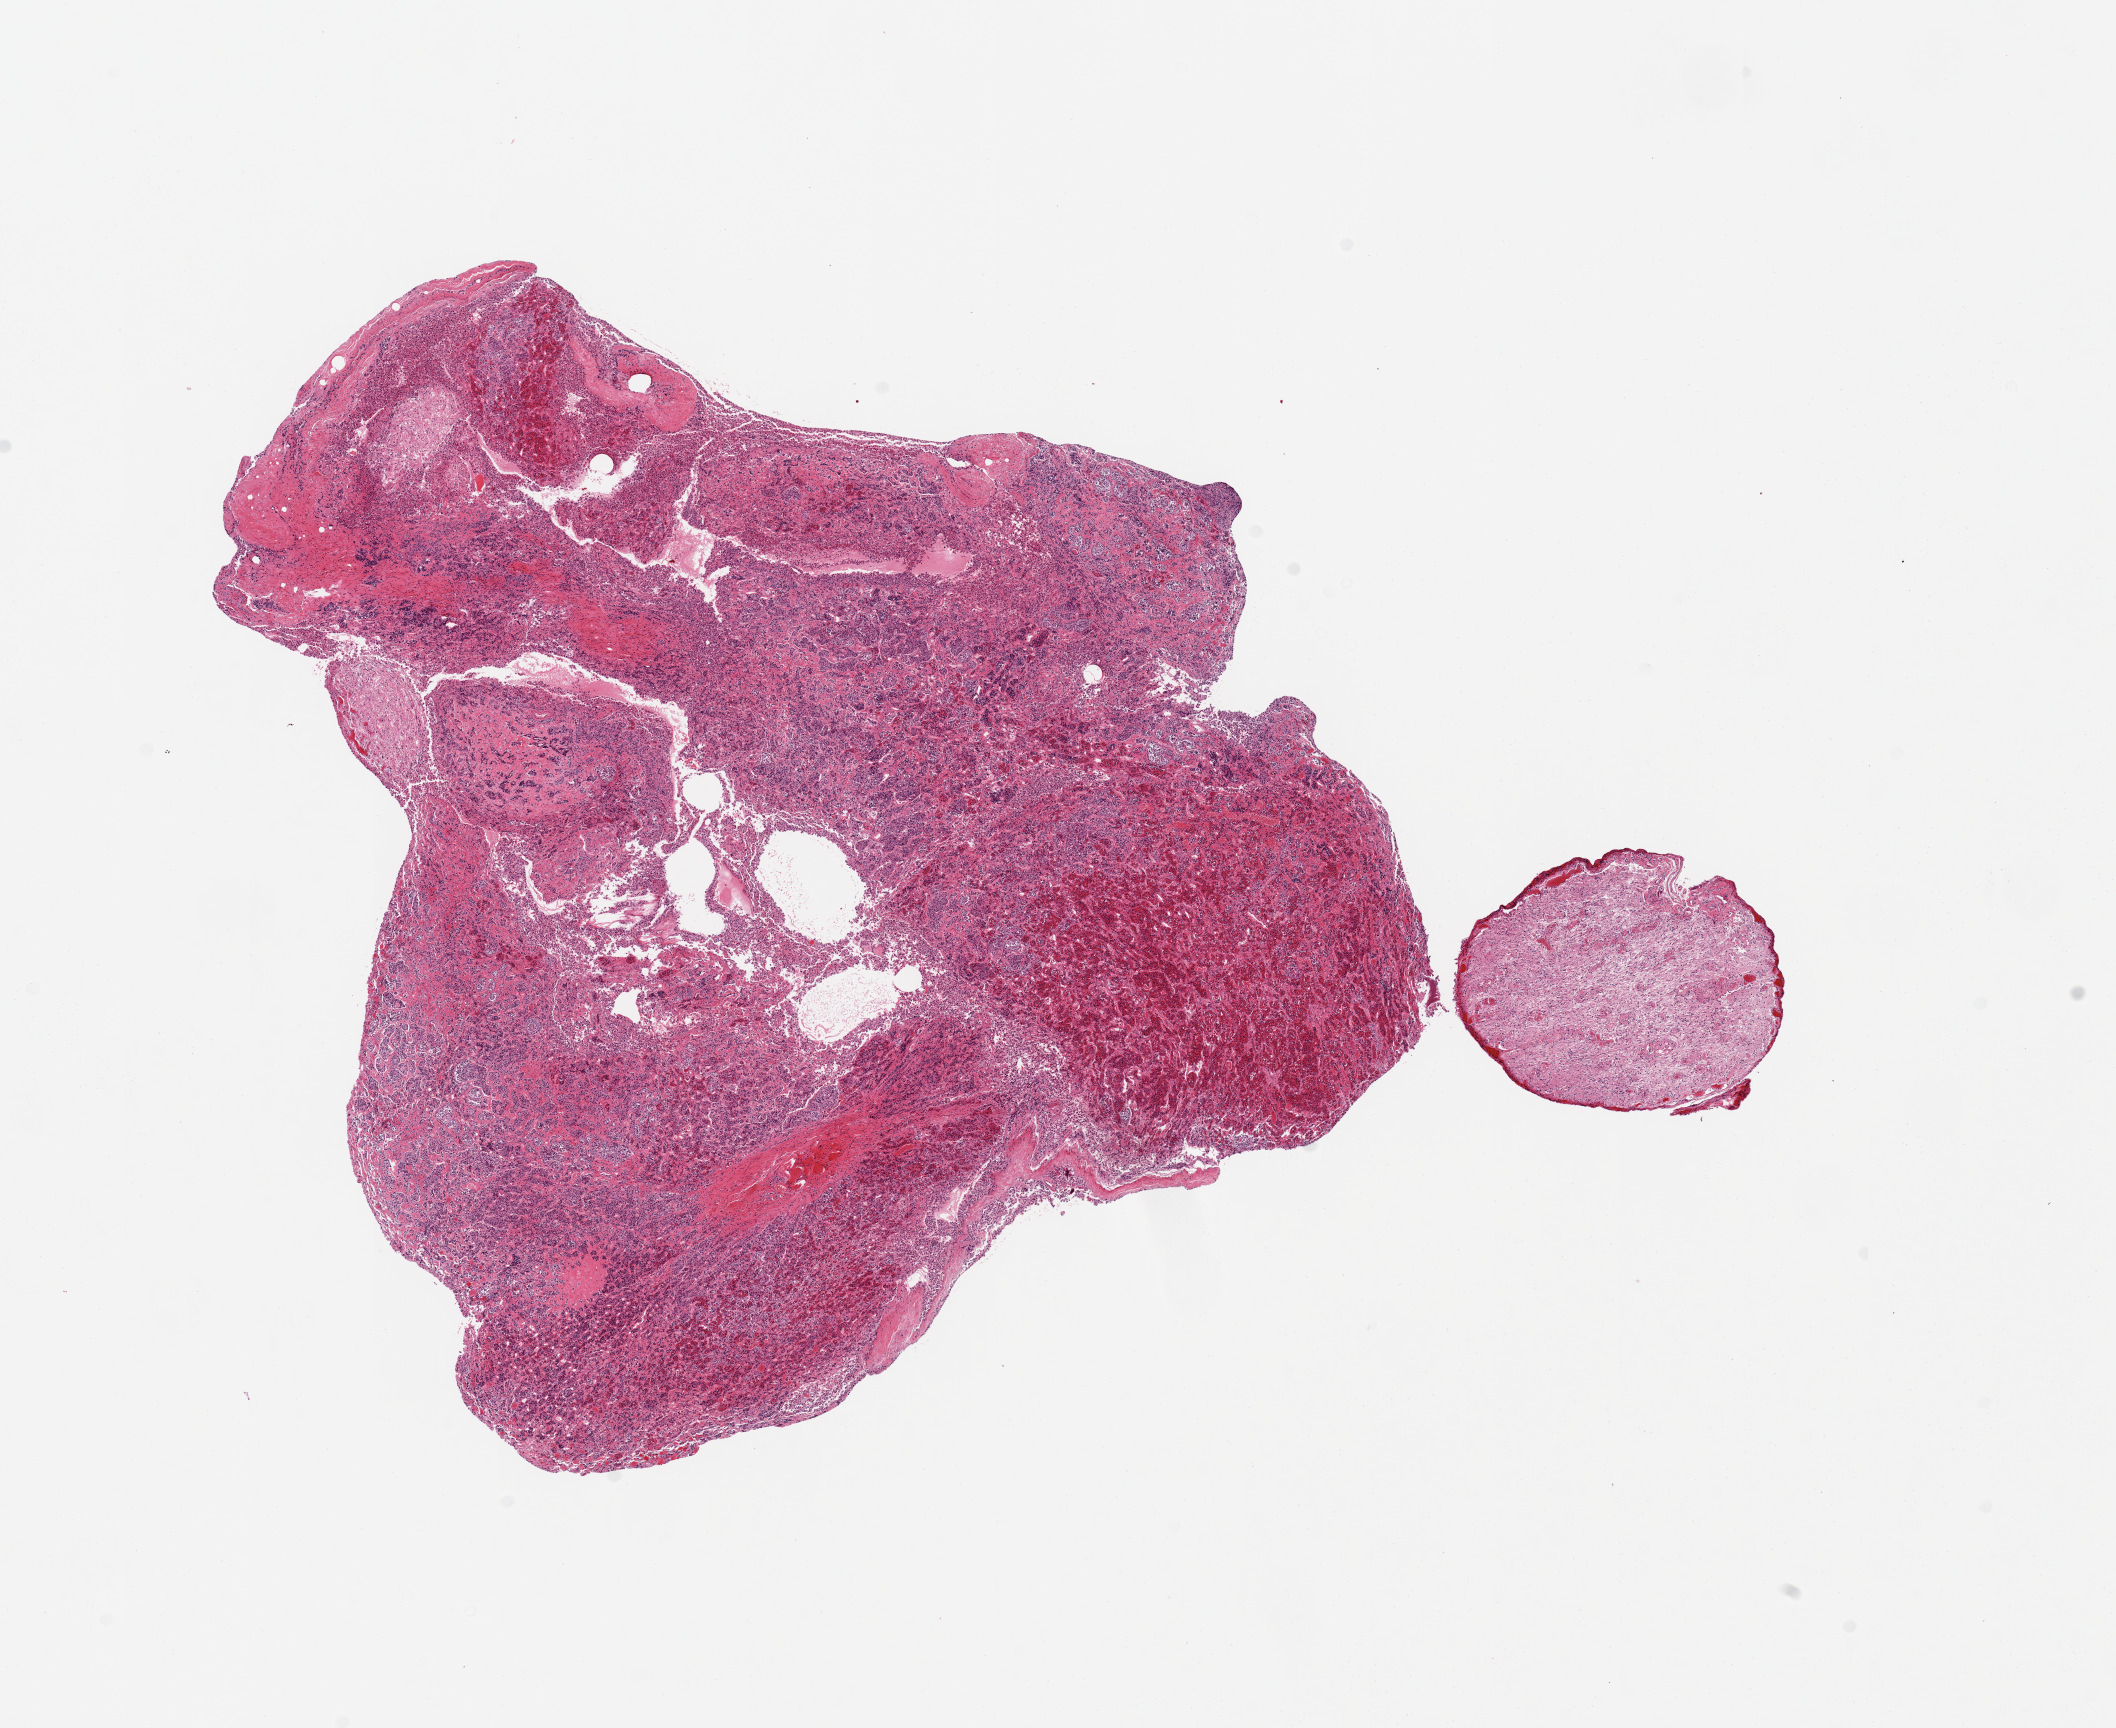
Digitized hematoxylin and eosin (H&E)-stained section — whole scanned area (about 16.7 x 13.7 mm) shown as a low-resolution overview. PAXgene-fixed paraffin-embedded (PFPE) section. Target tissue: pituitary. Donor tissue sample. Donor sex: female.
- pathologist's review note for this sample: 1 piece; mostly anterior; neurohypophysis marked